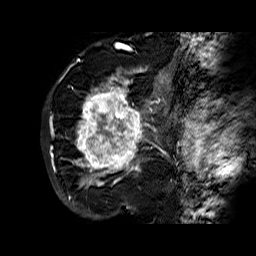
Breast MRI (dynamic contrast-enhanced), one sagittal slice. Slice 43 of 60 in the series (ordered by position). Dynamic contrast-enhanced series, time point 2 of 6 at this slice position (early post-contrast). 1.5 T. TE 6.3 ms, TR 32.4 ms. 4 mm slice thickness. 256 × 256 image matrix. Female patient. From the clinical record (not read from this slice): setting: breast cancer imaged before/during neoadjuvant chemotherapy; receptor status: HR-positive, HER2-negative.
Structures marked on this image (semi-automatic segmentation, software-assisted and operator-edited):
- analysis volume of interest (the breast-tissue region the enhancement analysis was run in; not a lesion): box from (x=68, y=72) to (x=177, y=183) px
- tumour enhancement mask (voxels above the 100 % enhancement threshold inside the analysis volume of interest): (x=75, y=72)–(x=167, y=183)